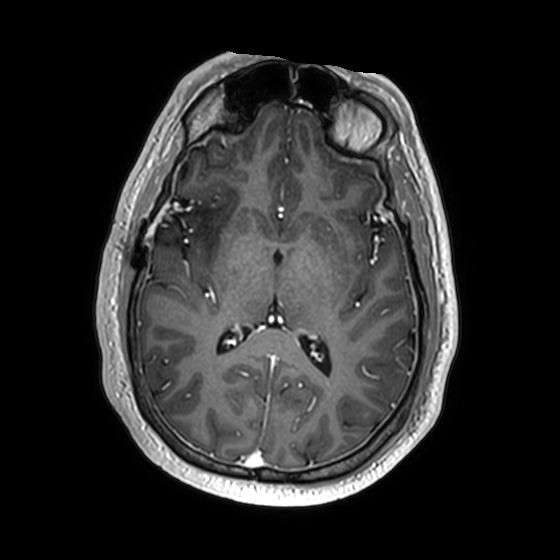
Brain MRI from a brain-tumour surgery series, one axial slice; slice 88 of 174 in the series (ordered by position); T1-weighted post-contrast; 560 × 560 image matrix. Case-level facts recorded for this patient, not image findings: histopathology: Astrocytoma; WHO grade: 2; IDH mutation: yes; tumour location: Right Insular.
Annotated regions visible in this slice (outlined manually by an expert reader):
- previous resection cavity: box from (x=176, y=198) to (x=188, y=208) px